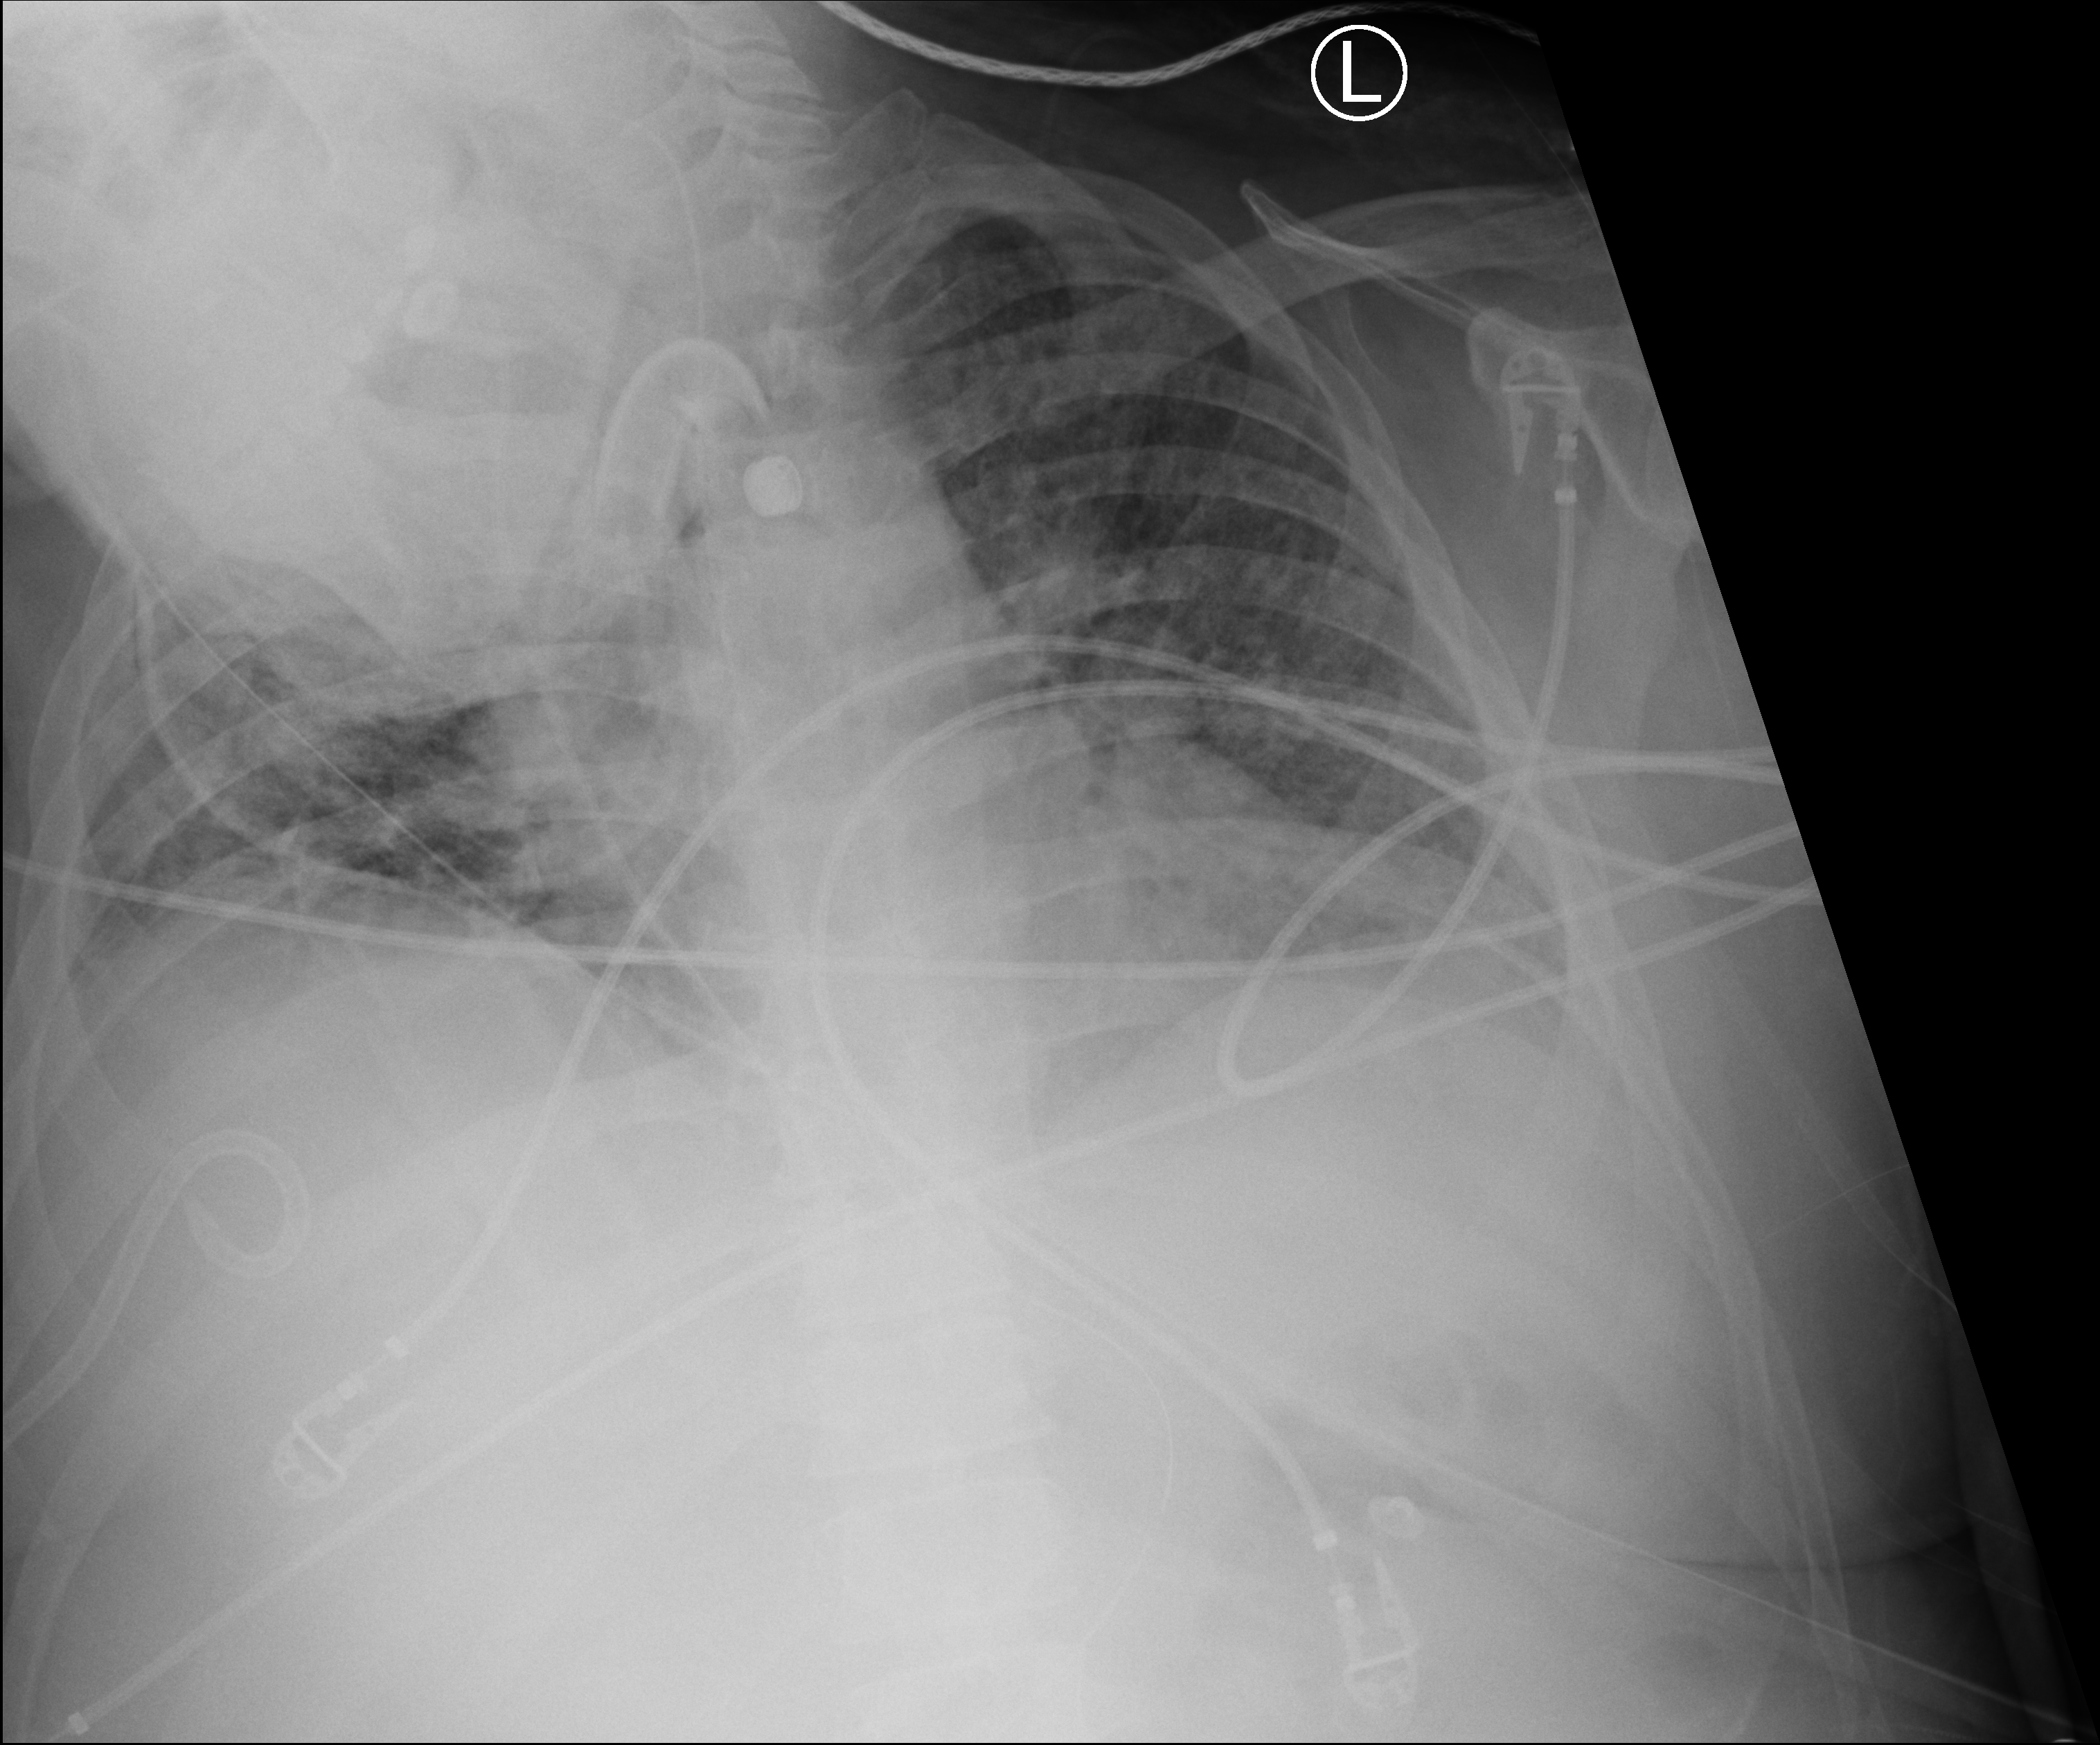
Portable chest radiograph, anteroposterior (AP) projection. Patient hospitalised with COVID-19; male, aged 18–59 years.
Admission-level facts for this patient (not findings on this image; timing relative to this image not recorded): hypertension (admission record): yes.